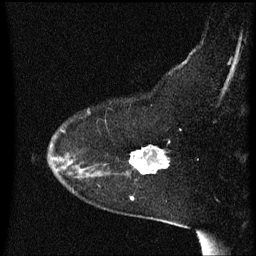
Breast MRI (dynamic contrast-enhanced), one sagittal slice. Dynamic contrast-enhanced series, image 2 of 3 at this slice position (ordered by acquisition). 1.5 T. TE 4.2 ms, TR 8.4 ms. 2 mm slice thickness. 256 × 256 image matrix. Patient: female, 54 years. Case-level facts recorded for this patient, not image findings: setting: breast cancer imaged before/during neoadjuvant chemotherapy; receptor status: HR-positive, HER2-negative.
Structures marked on this image (semi-automatic segmentation, software-assisted and operator-edited):
- analysis volume of interest (the breast-tissue region the enhancement analysis was run in; not a lesion): box from (x=117, y=146) to (x=171, y=185) px
- tumour enhancement mask (voxels above the 70 % enhancement threshold inside the analysis volume of interest): (x=131, y=146)–(x=170, y=175)